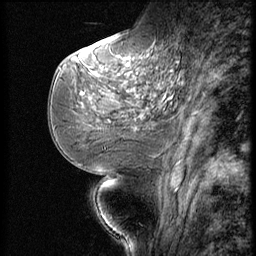
Breast MRI (dynamic contrast-enhanced), one sagittal slice; slice 24 of 56 in the series (ordered by position); dynamic contrast-enhanced series, image 2 of 3 at this slice position (ordered by acquisition); 1.5 T; TE 4.2 ms, TR 9 ms; 256 × 256 image matrix, field of view 180 × 180 mm. Patient: female, 51 years. From the clinical record (not read from this slice): setting: breast cancer imaged before/during neoadjuvant chemotherapy; receptor status: triple-negative.
Annotated regions visible in this slice (semi-automatic segmentation, software-assisted and operator-edited):
- analysis volume of interest (the breast-tissue region the enhancement analysis was run in; not a lesion): bounding box <73,46,172,147> (left, top, right, bottom; pixels)
- tumour enhancement mask (voxels above the 140 % enhancement threshold inside the analysis volume of interest): <127,64,130,67>